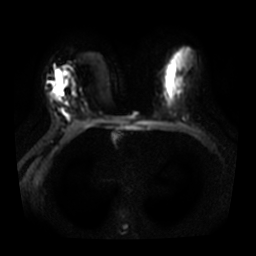
Breast MRI, one axial slice. Slice 18 of 31 in the series (ordered by position). Diffusion-weighted series; image 2 of 4 stored at this slice position (different b-values; order by instance number). 3 T. 5 mm slice thickness. 256 × 256 image matrix. Female patient.
Structures marked on this image (expert manual segmentation):
- tumour on diffusion-weighted imaging: bounding box (x1, y1, x2, y2) in pixels: (56, 70, 62, 94)